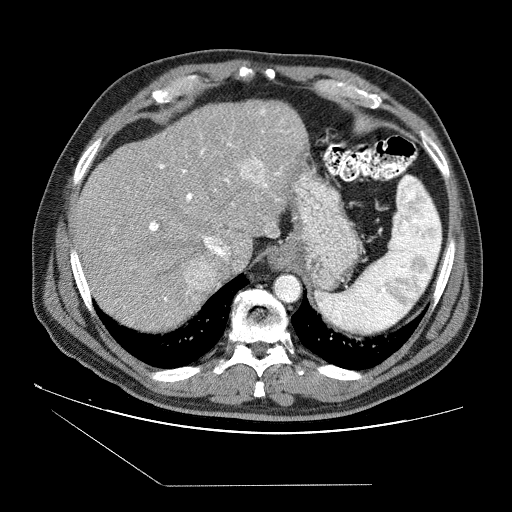
Contrast-enhanced abdominal CT (liver protocol), one axial slice; slice 63 of 87 in the series (ordered by position); reconstruction kernel STANDARD; 120 kVp; soft-tissue window (W 400 / L 40 HU); 2.5 mm slice thickness; 512 × 512 image matrix, field of view 400 × 400 mm. Case-level facts recorded for this patient, not image findings: diagnosis: hepatocellular carcinoma (patient treated with transarterial chemoembolisation; whether this scan precedes or follows treatment is not stated here); TNM stage (as recorded): Stage-II; Child-Pugh class: B; tumour differentiation: no biopsy; tumour size: 2.6 cm.
Structures marked on this image (semi-automatically segmented with operator editing):
- liver parenchyma outside the tumour (the mass and vessels are separate outlines, so this box may not span the whole liver): bounding box [x1, y1, x2, y2] px = [74, 100, 308, 330]
- mass: [184, 158, 266, 291]
- liver vessels: [112, 108, 289, 325]